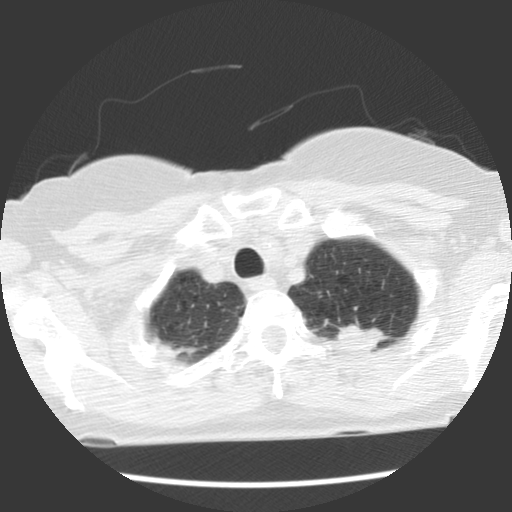
Low-dose screening chest CT, axial slice. Baseline annual screen. Lung window (W 1500 / L -600 HU). Slice 103 of 120 in the series. Female, age 66 years at enrolment. Former smoker at enrolment.
Lesion marked by an expert reader, bounding box <316,303,385,361> (left, top, right, bottom; pixels). Screening reader's record for this exam (one nodule recorded; not confirmed to be the boxed lesion): non-calcified nodule or mass ≥4 mm, left upper lobe, 22 × 17 mm, spiculated (stellate) margins, soft tissue attenuation. Official screen result: positive, change unspecified: nodule(s) >= 4 mm or enlarging nodule(s), mass(es), or other non-specific abnormalities suspicious for lung cancer. Later outcome: lung cancer diagnosed 50 days after this screen — adenocarcinoma, NOS, left upper lobe, poorly differentiated (G3), stage IB (AJCC 6th edition), 40 mm at pathology.